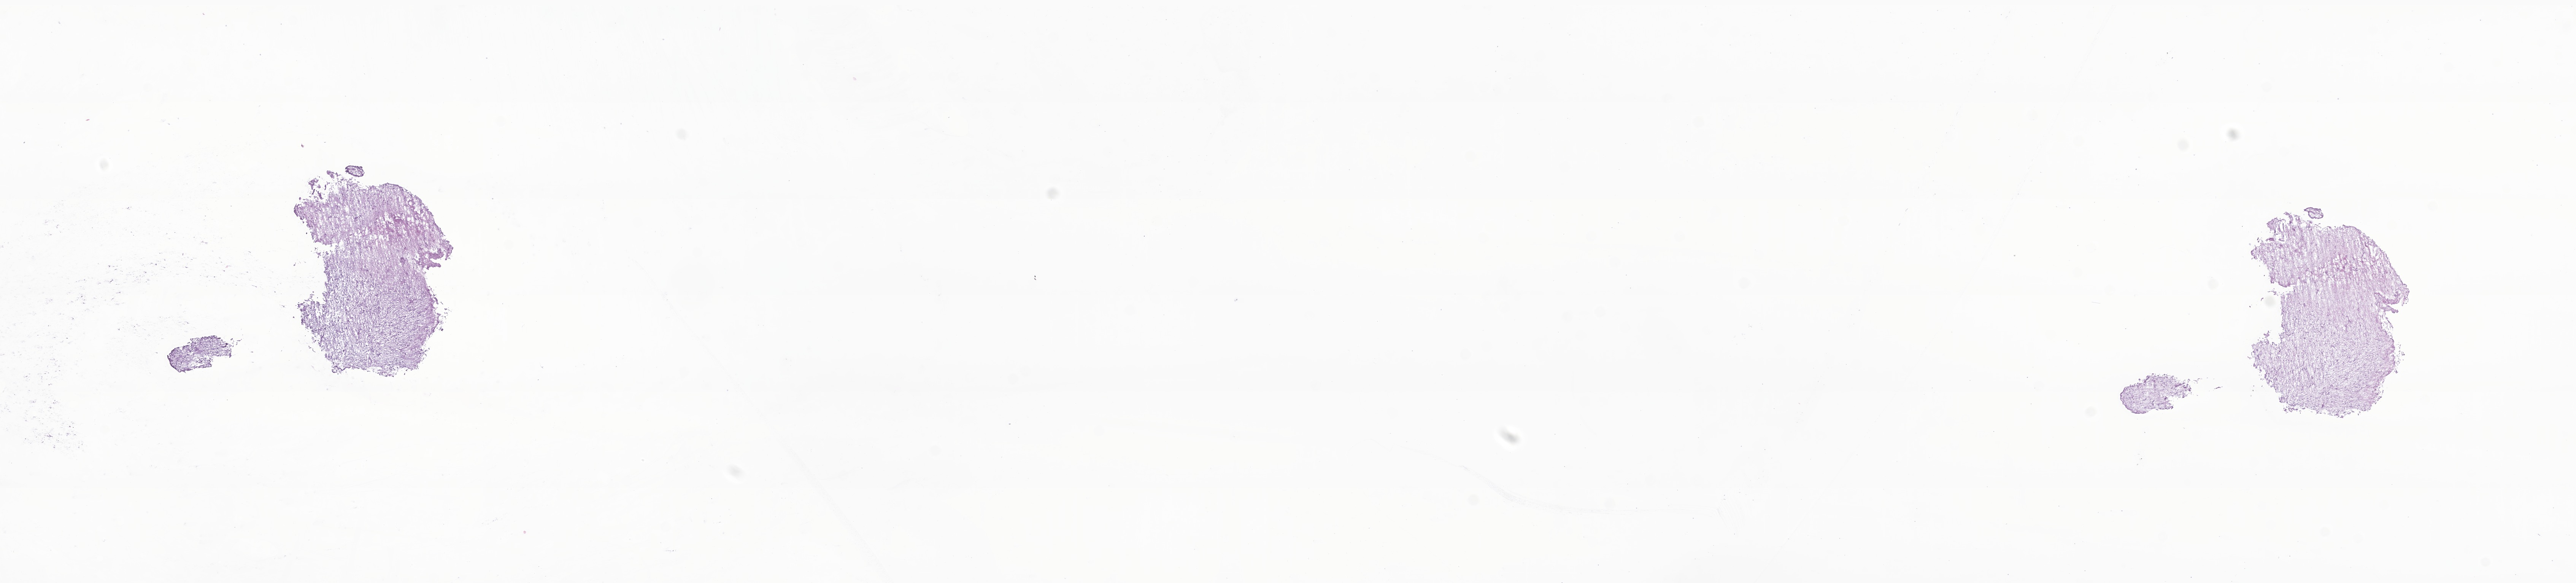
Whole-slide image, H&E stain of tumor tissue from the brain — whole scanned area (about 28.6 x 6.5 mm) shown as a low-resolution overview, cryosection (OCT / tissue freezing medium). Patient: male, age 41 months.
* diagnosis (ICD-O-3 morphology term): Neoplasm, malignant